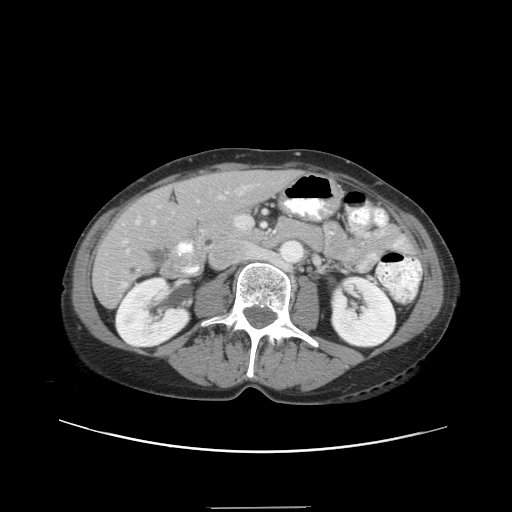
Contrast-enhanced abdominal CT, one axial slice. Position 13 of 38 along the scan axis. 120 kVp. Intravenous contrast given. Soft-tissue window (W 400 / L 40 HU). 5 mm slice thickness. 512 × 512 image matrix, field of view 388 × 388 mm. Female patient, age 64 years. From the clinical record (not read from this slice): diagnosis: colorectal cancer liver metastases, imaged before liver resection; multiple liver metastases: no; largest metastasis: 3.8 cm; disease in both lobes: yes.
Outlined on this slice (expert manual segmentation):
- hepatic veins: box from (x=123, y=192) to (x=243, y=244) px
- liver: (x=94, y=171)–(x=298, y=304)
- planned liver remnant (the part of the liver to remain after resection): (x=148, y=171)–(x=298, y=230)
- portal vein (with intrahepatic branches): (x=122, y=191)–(x=228, y=253)